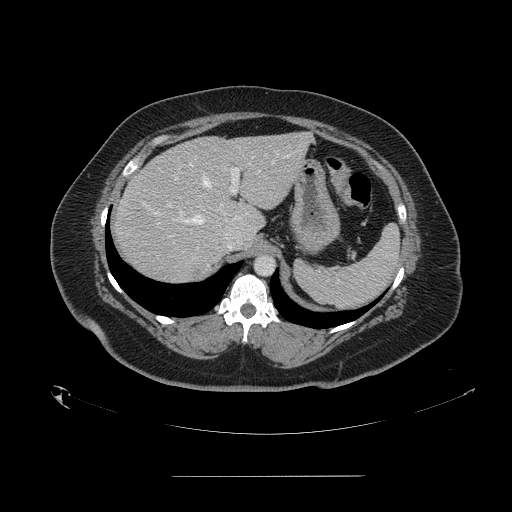
Contrast-enhanced abdominal CT, one axial slice; position 111 of 164 along the scan axis; 120 kVp; intravenous contrast given; soft-tissue window (W 400 / L 40 HU); 2.5 mm slice thickness; 512 × 512 image matrix. Female patient, age 52 years. Case-level facts recorded for this patient, not image findings: diagnosis: colorectal cancer liver metastases, imaged before liver resection; multiple liver metastases: yes; largest metastasis: 3.5 cm; disease in both lobes: no.
Outlined on this slice (manually delineated by an expert):
- hepatic veins: bounding box <153,155,289,224> (left, top, right, bottom; pixels)
- liver: <113,133,311,284>
- planned liver remnant (the part of the liver to remain after resection): <171,133,311,229>
- portal vein (with intrahepatic branches): <168,163,250,214>